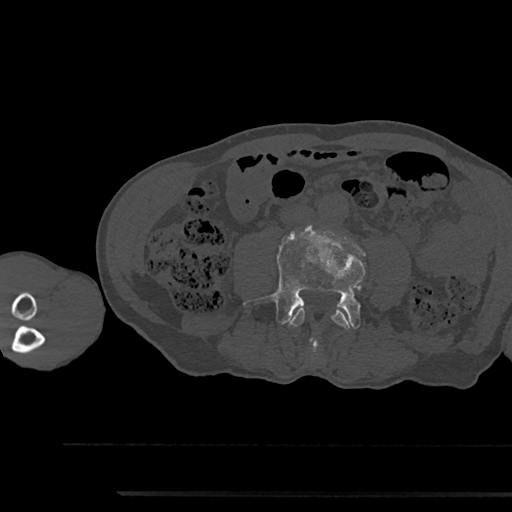
CT including the spine, one axial slice. Slice 436 of 797 in the series (ordered by position). Reconstruction kernel Br40s/3. 120 kVp. Bone window (W 1800 / L 400 HU). 0.5 mm slice thickness. 512 × 512 image matrix. Male patient, age 79 years. Case-level facts recorded for this patient, not image findings: primary cancer: prostate.
Outlined on this slice (semi-automatically segmented with operator editing):
- L3 vertebra: bounding box <289,306,351,330> (left, top, right, bottom; pixels)
- L4 vertebra: <244,226,365,351>